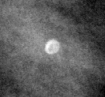
Cropped region of a digitized screen-film mammogram centred on a radiologist-marked abnormality; left breast; CC view.
Finding: calcifications, morphology lucent center; BI-RADS assessment category 2; benign without callback (not worked up further).